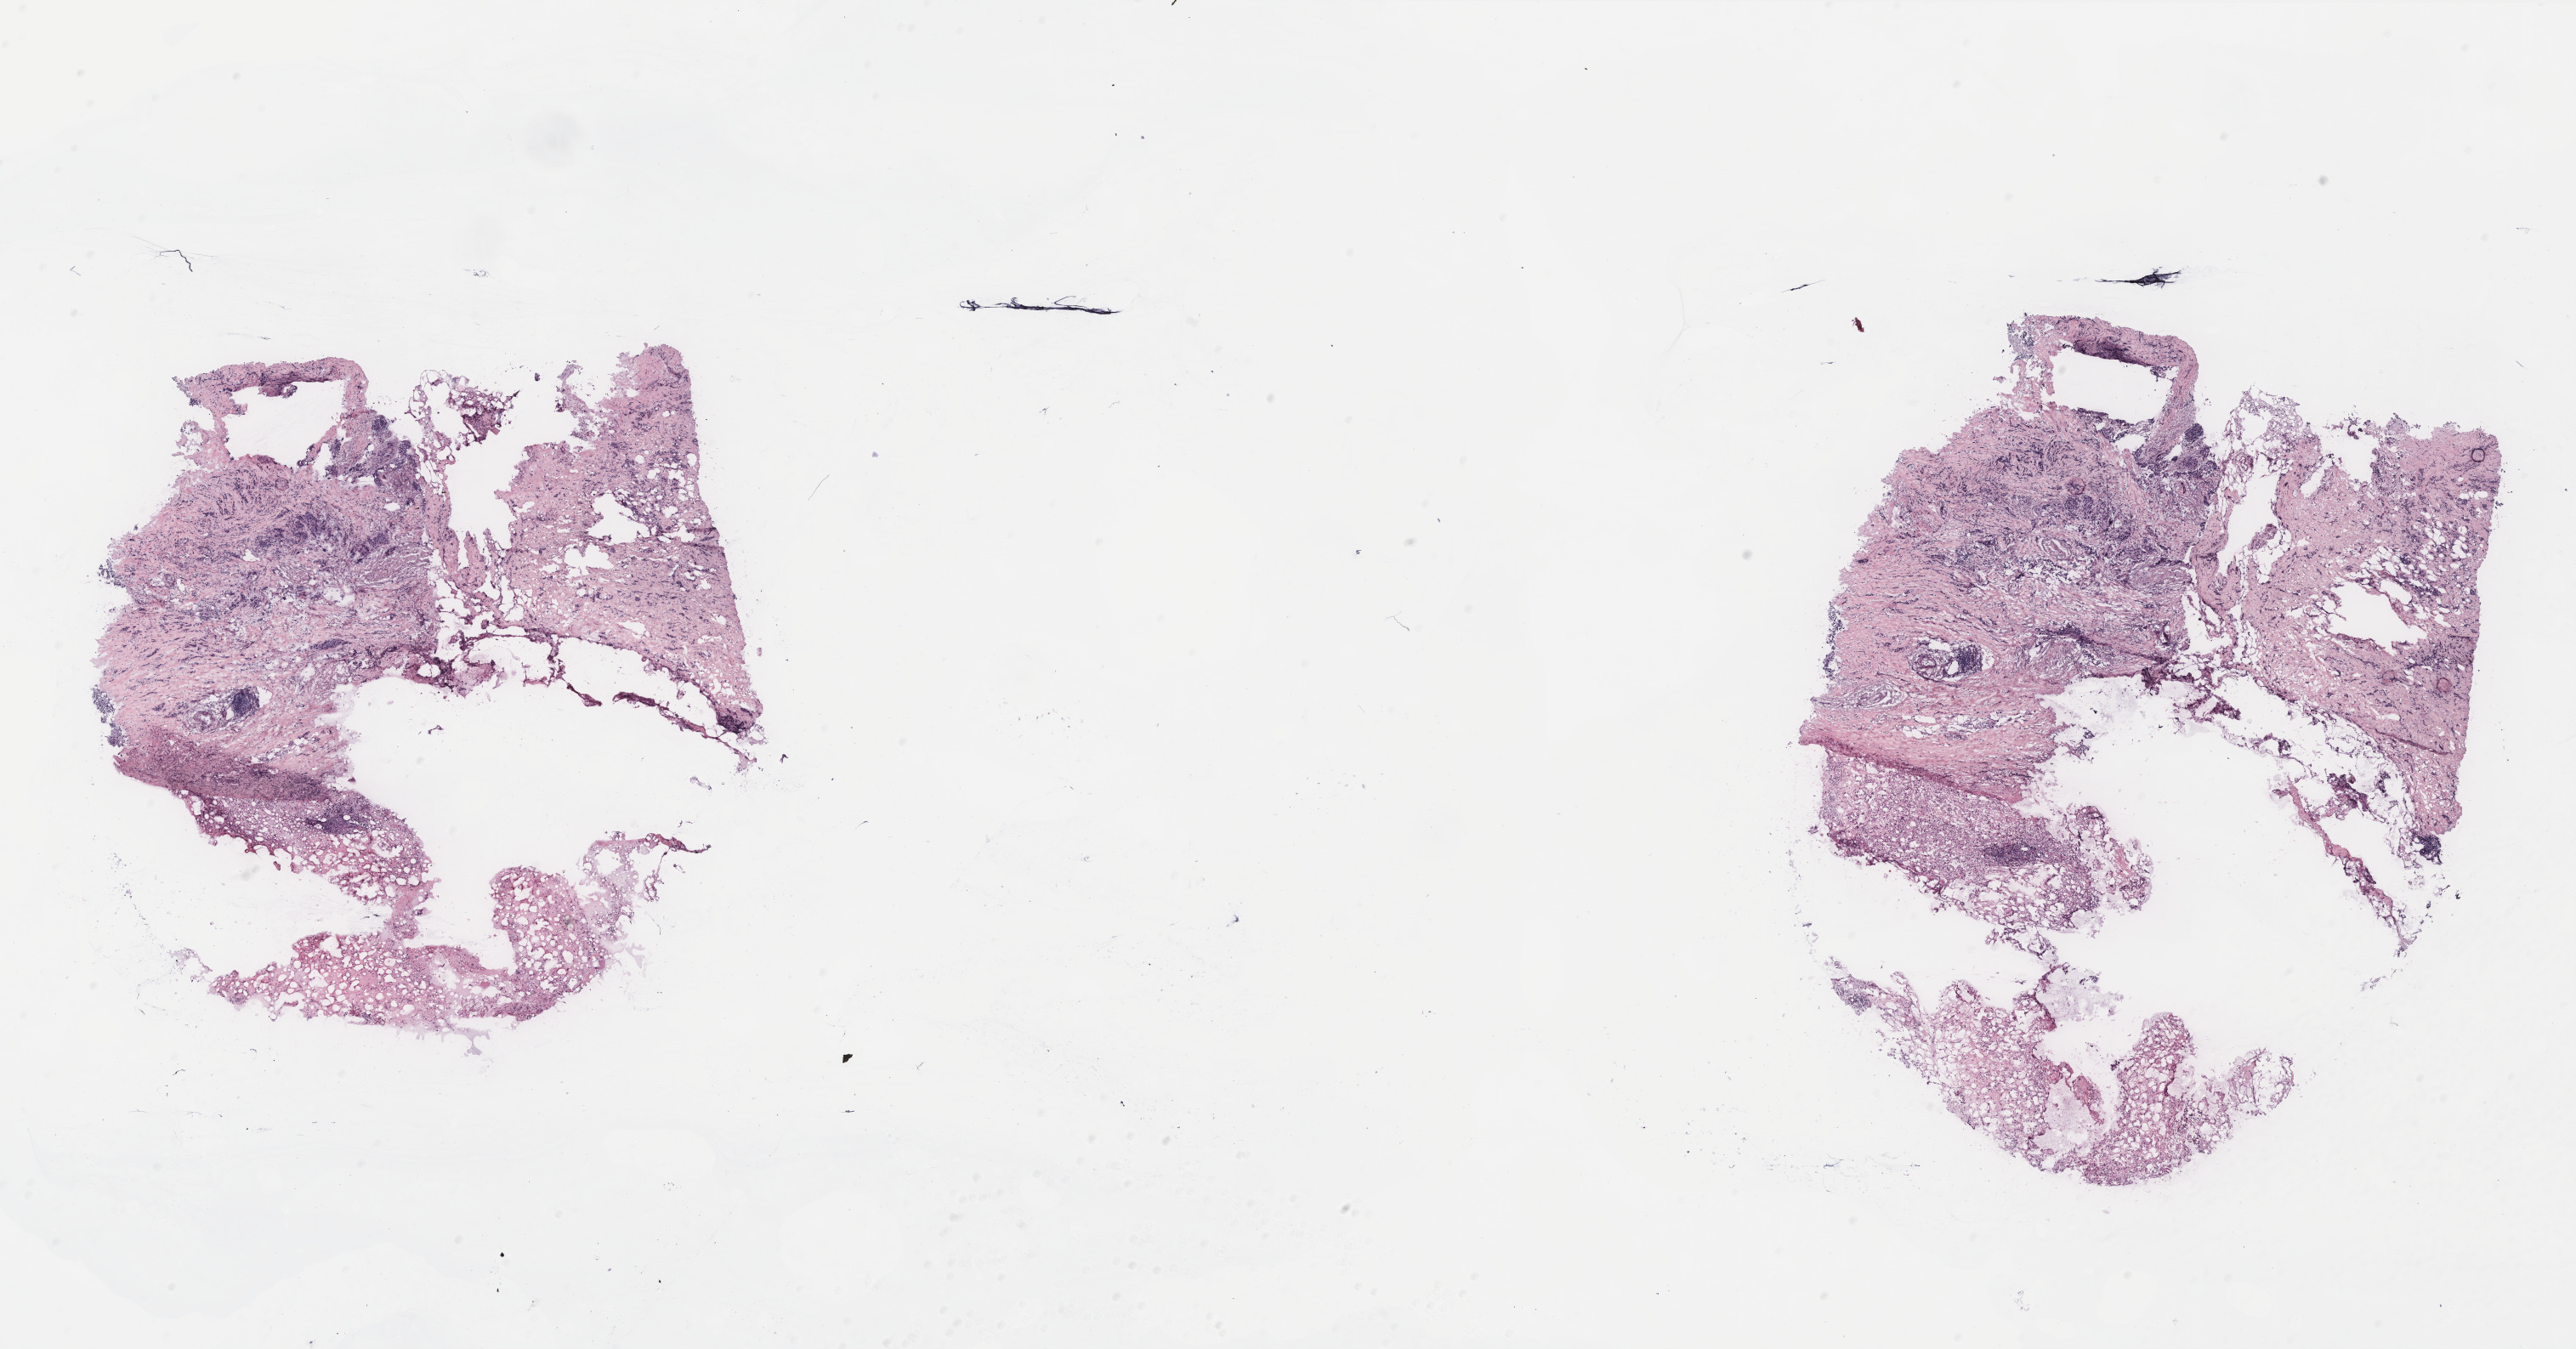
Digitized Hematoxylin and eosin (H&E) stained tissue section (whole slide), low-resolution overview of the scanned area, about 24.2 x 12.7 mm, breast, tissue type not recorded.
Patient diagnosis (cohort enrolment): breast cancer (breast).